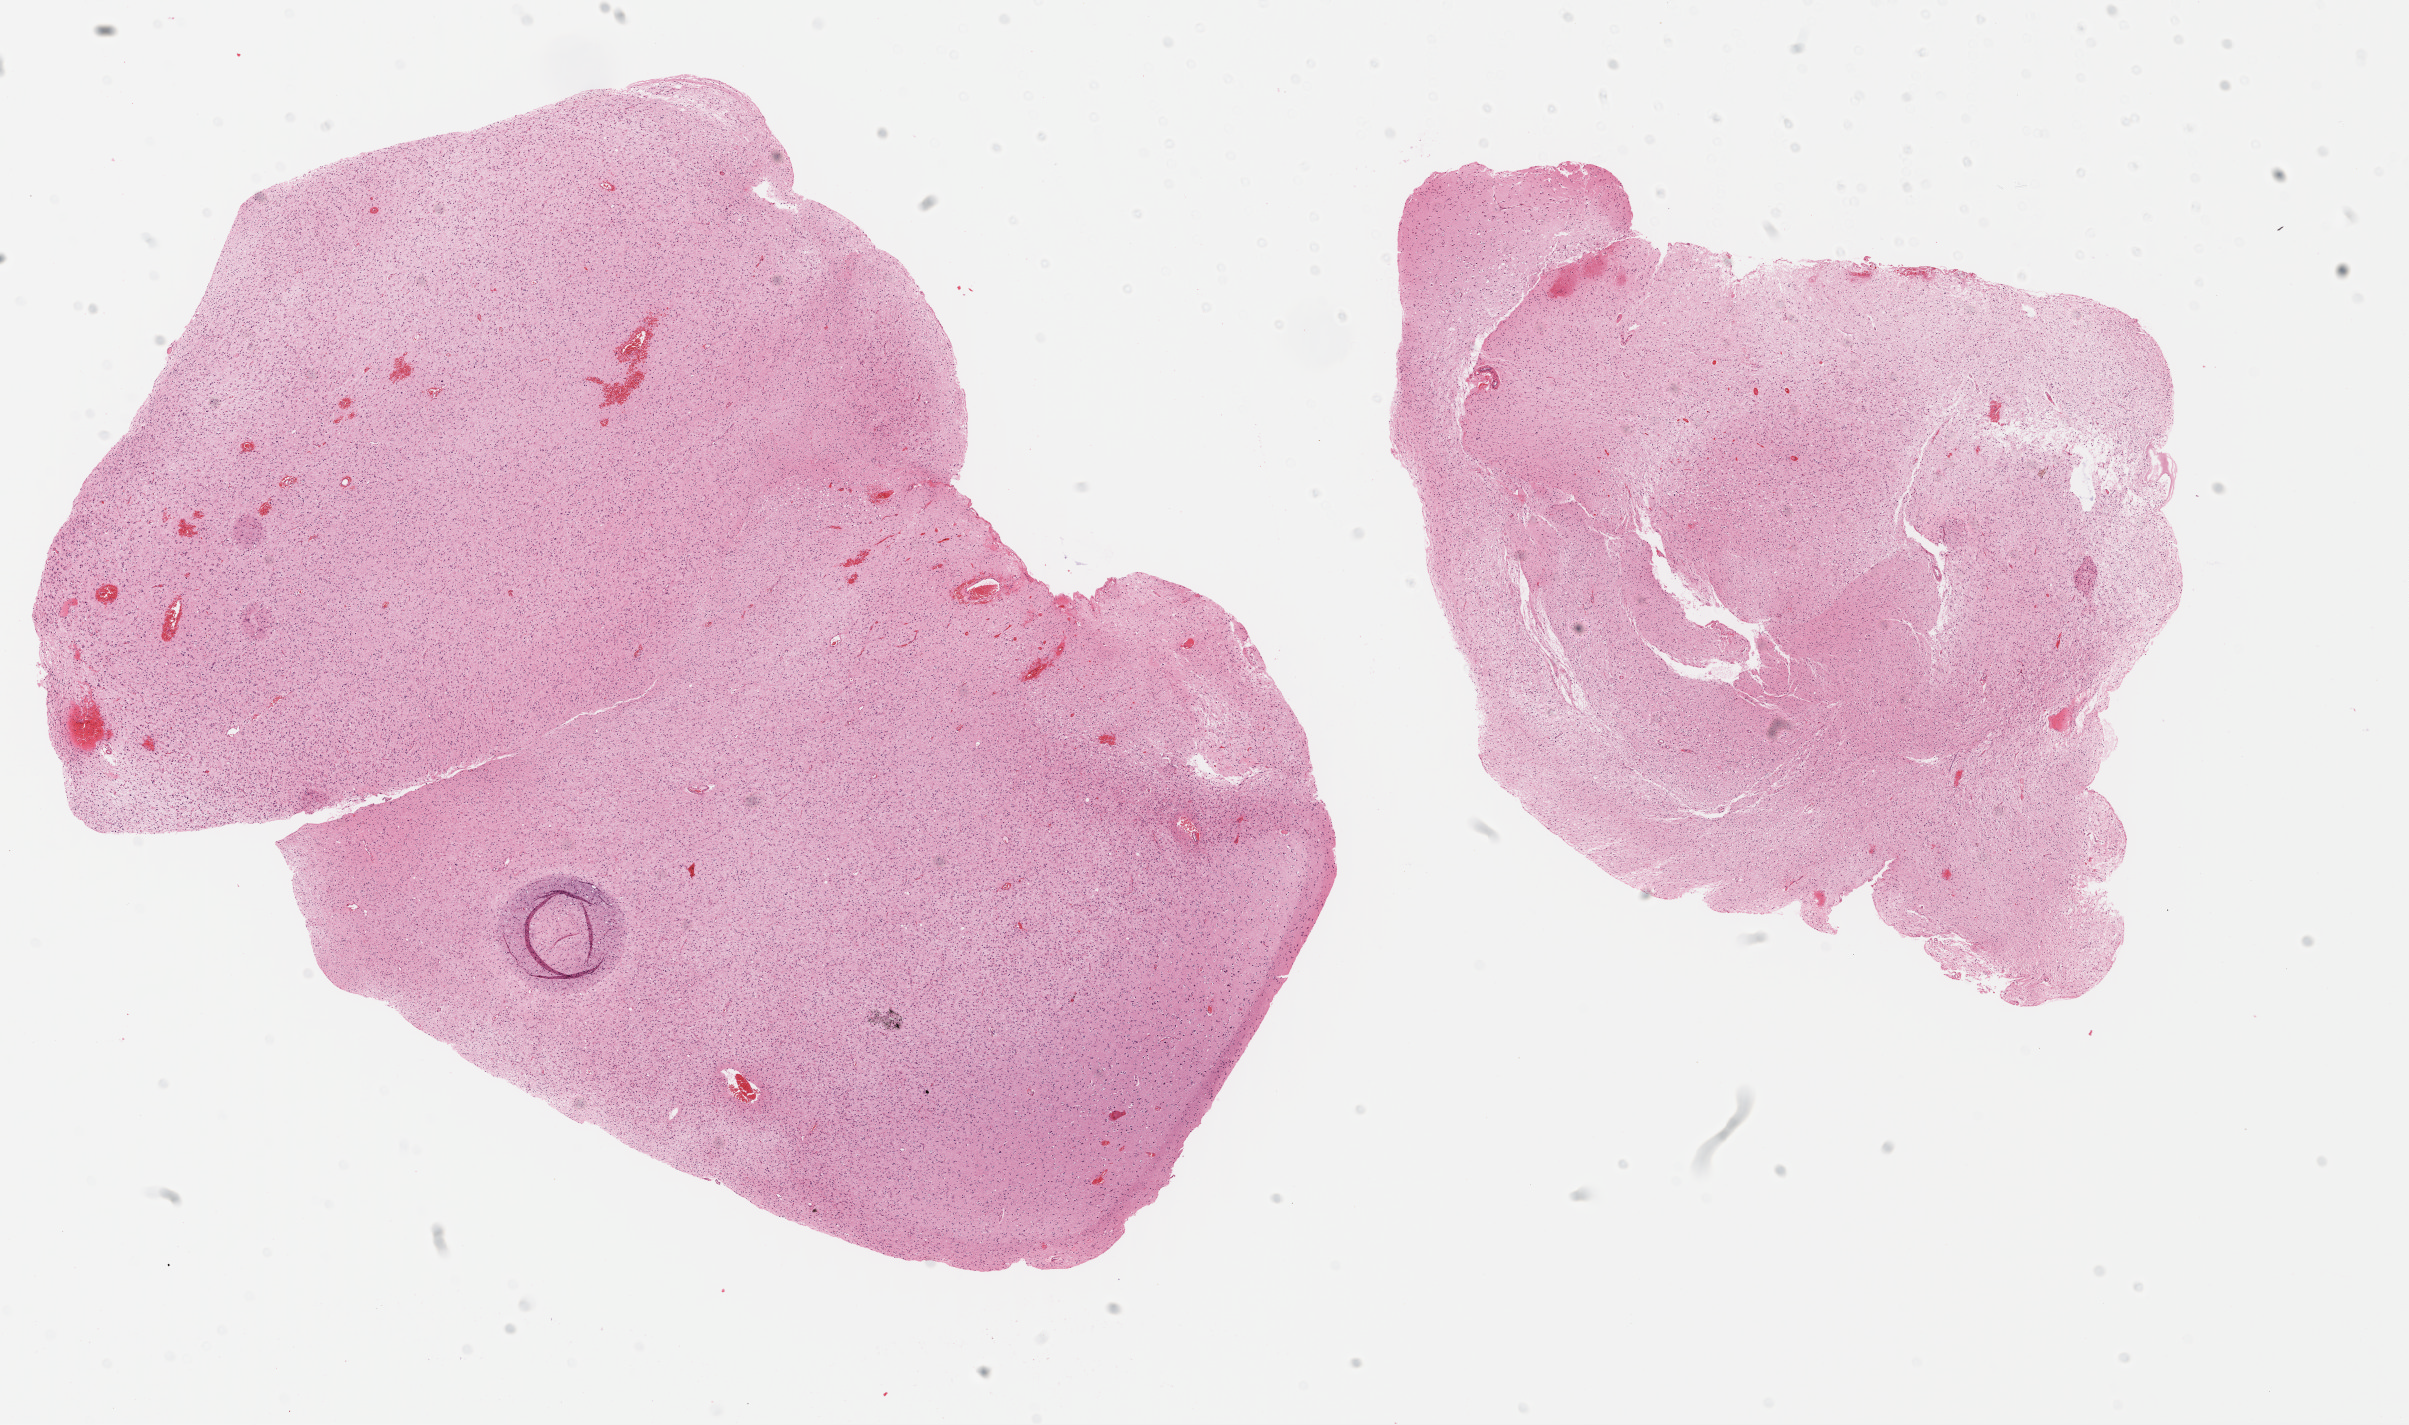
H&E whole-slide image, whole scanned area (about 18.9 x 11.2 mm) shown as a low-resolution overview. Formalin-fixed paraffin-embedded (FFPE) diagnostic section. Sample: primary tumour, brain. Patient: female, age at initial diagnosis 34 years. Histologic grade: G2 (moderately differentiated).
Diagnosis: Astrocytoma, NOS (cerebrum). Laterality: left.